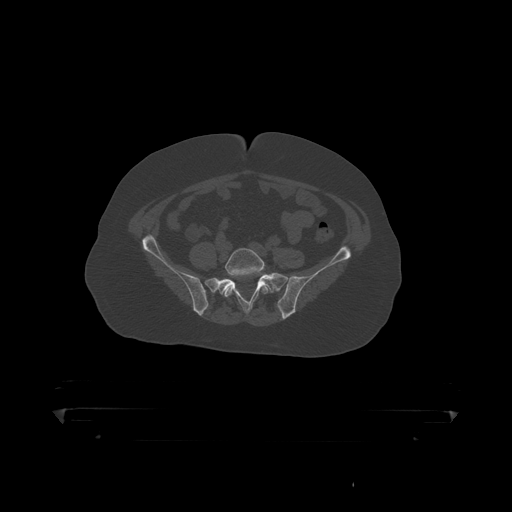
CT including the spine, one axial slice. Position 29 of 390 along the scan axis. 120 kVp. Bone window (W 1800 / L 400 HU). 1.25 mm slice thickness. 512 × 512 image matrix, field of view 650 × 650 mm. Male patient, age 60 years. From the clinical record (not read from this slice): primary cancer: prostate.
Annotated regions visible in this slice (semi-automatic segmentation, software-assisted and operator-edited):
- L5 vertebra: bounding box <224,248,270,298> (left, top, right, bottom; pixels)